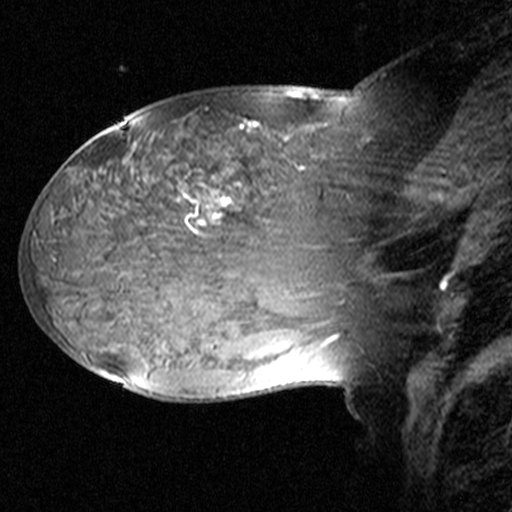
Breast MRI (dynamic contrast-enhanced), one sagittal slice. Dynamic contrast-enhanced study with each time point stored as its own series, time point 2 of 3 at this slice position (early post-contrast, ordered by acquisition time). 1.5 T. TE 4.5 ms, TR 11 ms. 3 mm slice thickness. 512 × 512 image matrix, field of view 240 × 240 mm. Female patient, age 38 years. From the clinical record (not read from this slice): setting: breast cancer imaged before/during neoadjuvant chemotherapy; receptor status: HR-positive, HER2-negative.
Annotated regions visible in this slice (semi-automatically segmented with operator editing):
- analysis volume of interest (the breast-tissue region the enhancement analysis was run in; not a lesion): bounding box [x1, y1, x2, y2] px = [124, 106, 405, 245]
- tumour enhancement mask (voxels above the 90 % enhancement threshold inside the analysis volume of interest): [200, 122, 251, 223]